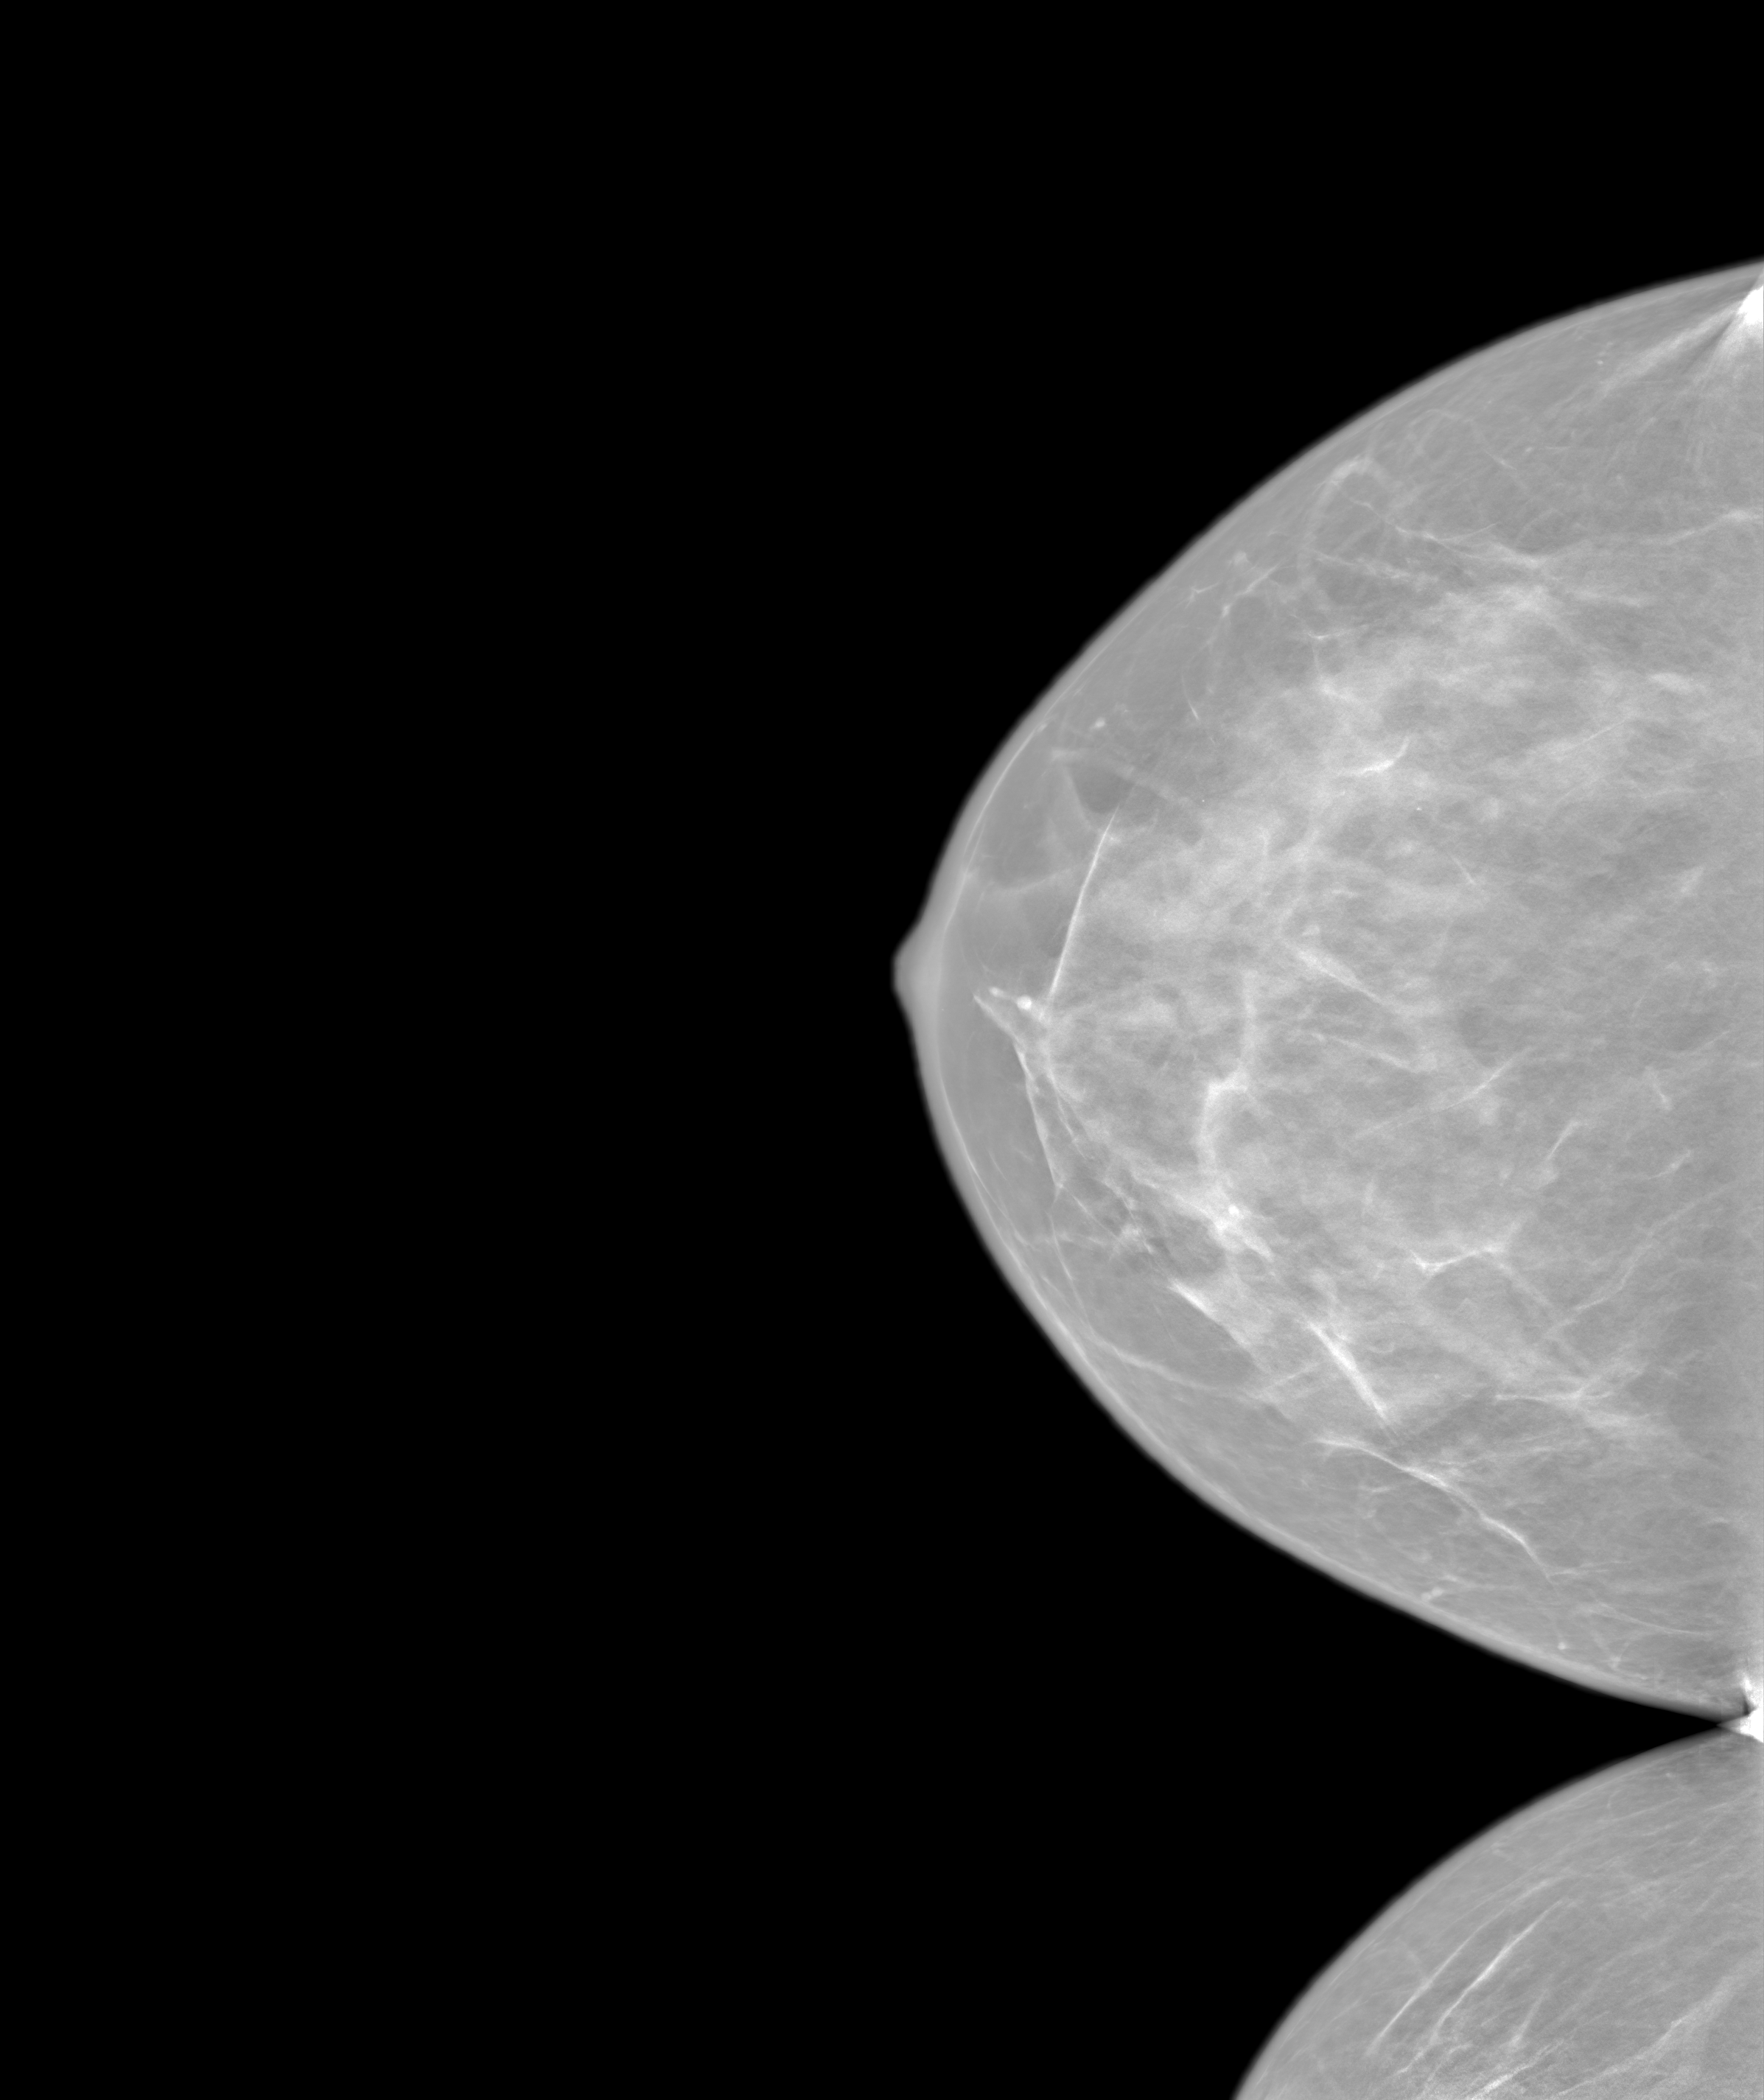
Annual screening mammography examination, system: SenoIris_1SP2(440). Patient aged 45 years (female).
Image type: synthesized 2-D view from tomosynthesis. Breast: right. Projection: craniocaudal (CC) view.